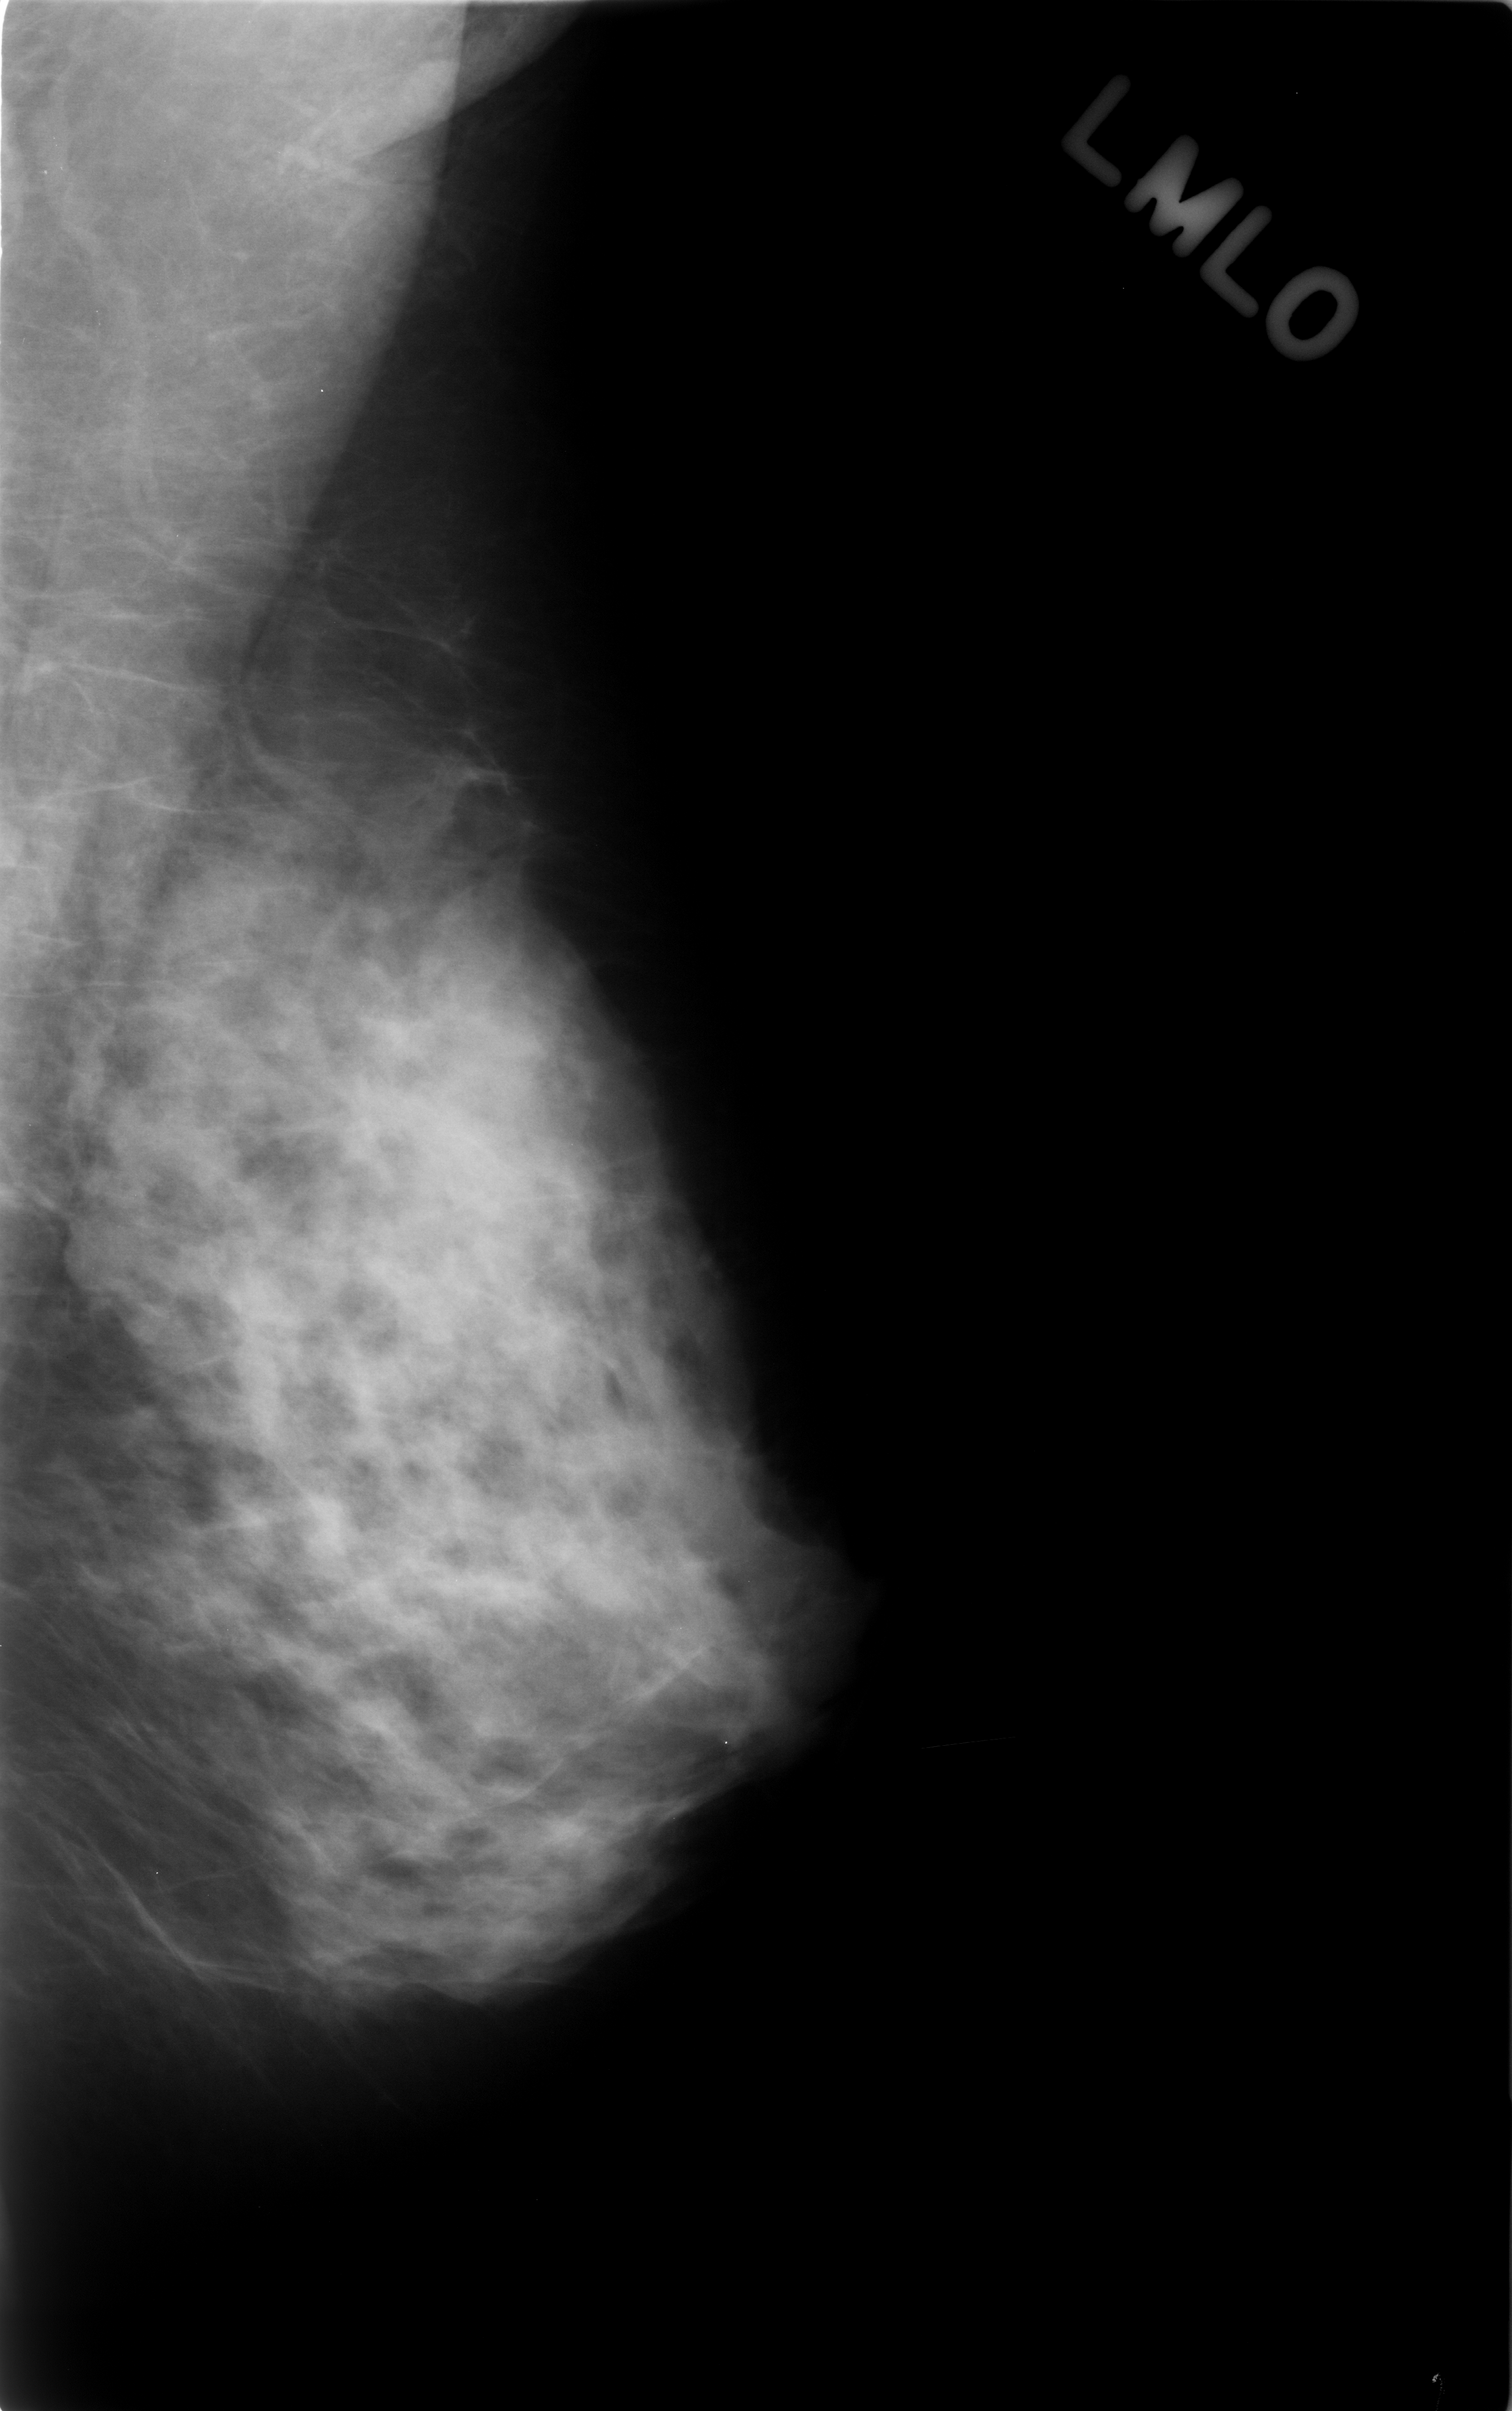
Scanned film-screen mammogram. Left breast. MLO view. 1512 × 2411 image matrix.
Expert-marked regions of interest on this image (one box per marked abnormality):
- mass, shape round, margins microlobulated; BI-RADS assessment category 3; outcome (as recorded, no biopsy): benign without callback (not worked up further): bounding box (x1, y1, x2, y2) in pixels: (46, 1137, 171, 1295)